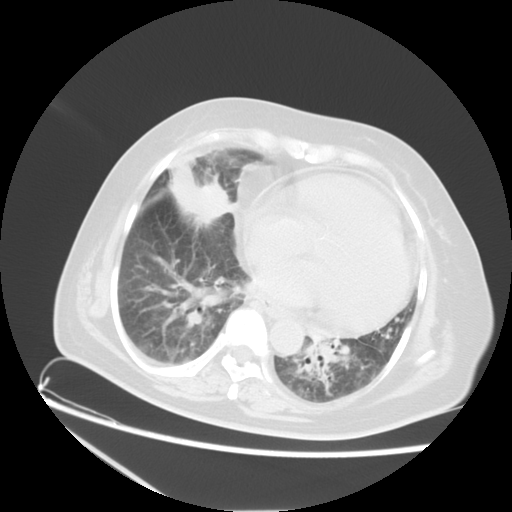
Chest CT, one axial slice; lung window (W 1500 / L -600 HU); 5 mm slice thickness; 512 × 512 image matrix, field of view 350 × 350 mm. Patient: female, 67 years. Case-level facts recorded for this patient, not image findings: clinical TNM (as recorded): T2a N3 M1a.
Outlined on this slice (bounding box drawn by a radiologist):
- lung tumour (recorded histology: adenocarcinoma): bounding box (x1, y1, x2, y2) in pixels: (166, 163, 231, 231)